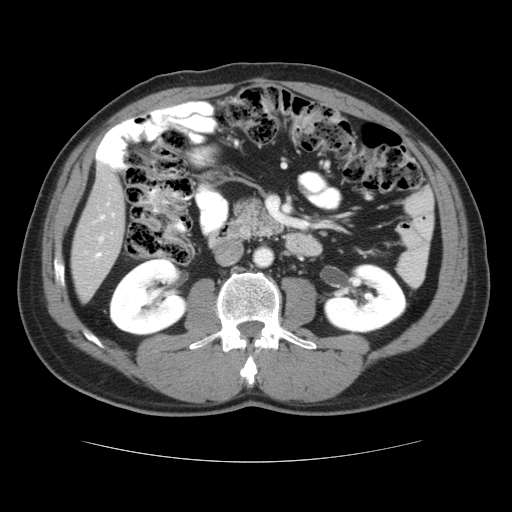
Contrast-enhanced abdominal CT, one axial slice; position 12 of 37 along the scan axis; 120 kVp; soft-tissue window (W 400 / L 40 HU); 512 × 512 image matrix, field of view 374 × 374 mm. Male patient, age 66 years. From the clinical record (not read from this slice): diagnosis: colorectal cancer liver metastases, imaged before liver resection; multiple liver metastases: yes; largest metastasis: 1.6 cm; disease in both lobes: yes.
Outlined on this slice (outlined manually by an expert reader):
- hepatic veins: box from (x=97, y=202) to (x=115, y=244) px
- liver: (x=72, y=162)–(x=126, y=301)
- planned liver remnant (the part of the liver to remain after resection): (x=72, y=177)–(x=126, y=301)
- portal vein (with intrahepatic branches): (x=96, y=217)–(x=103, y=257)